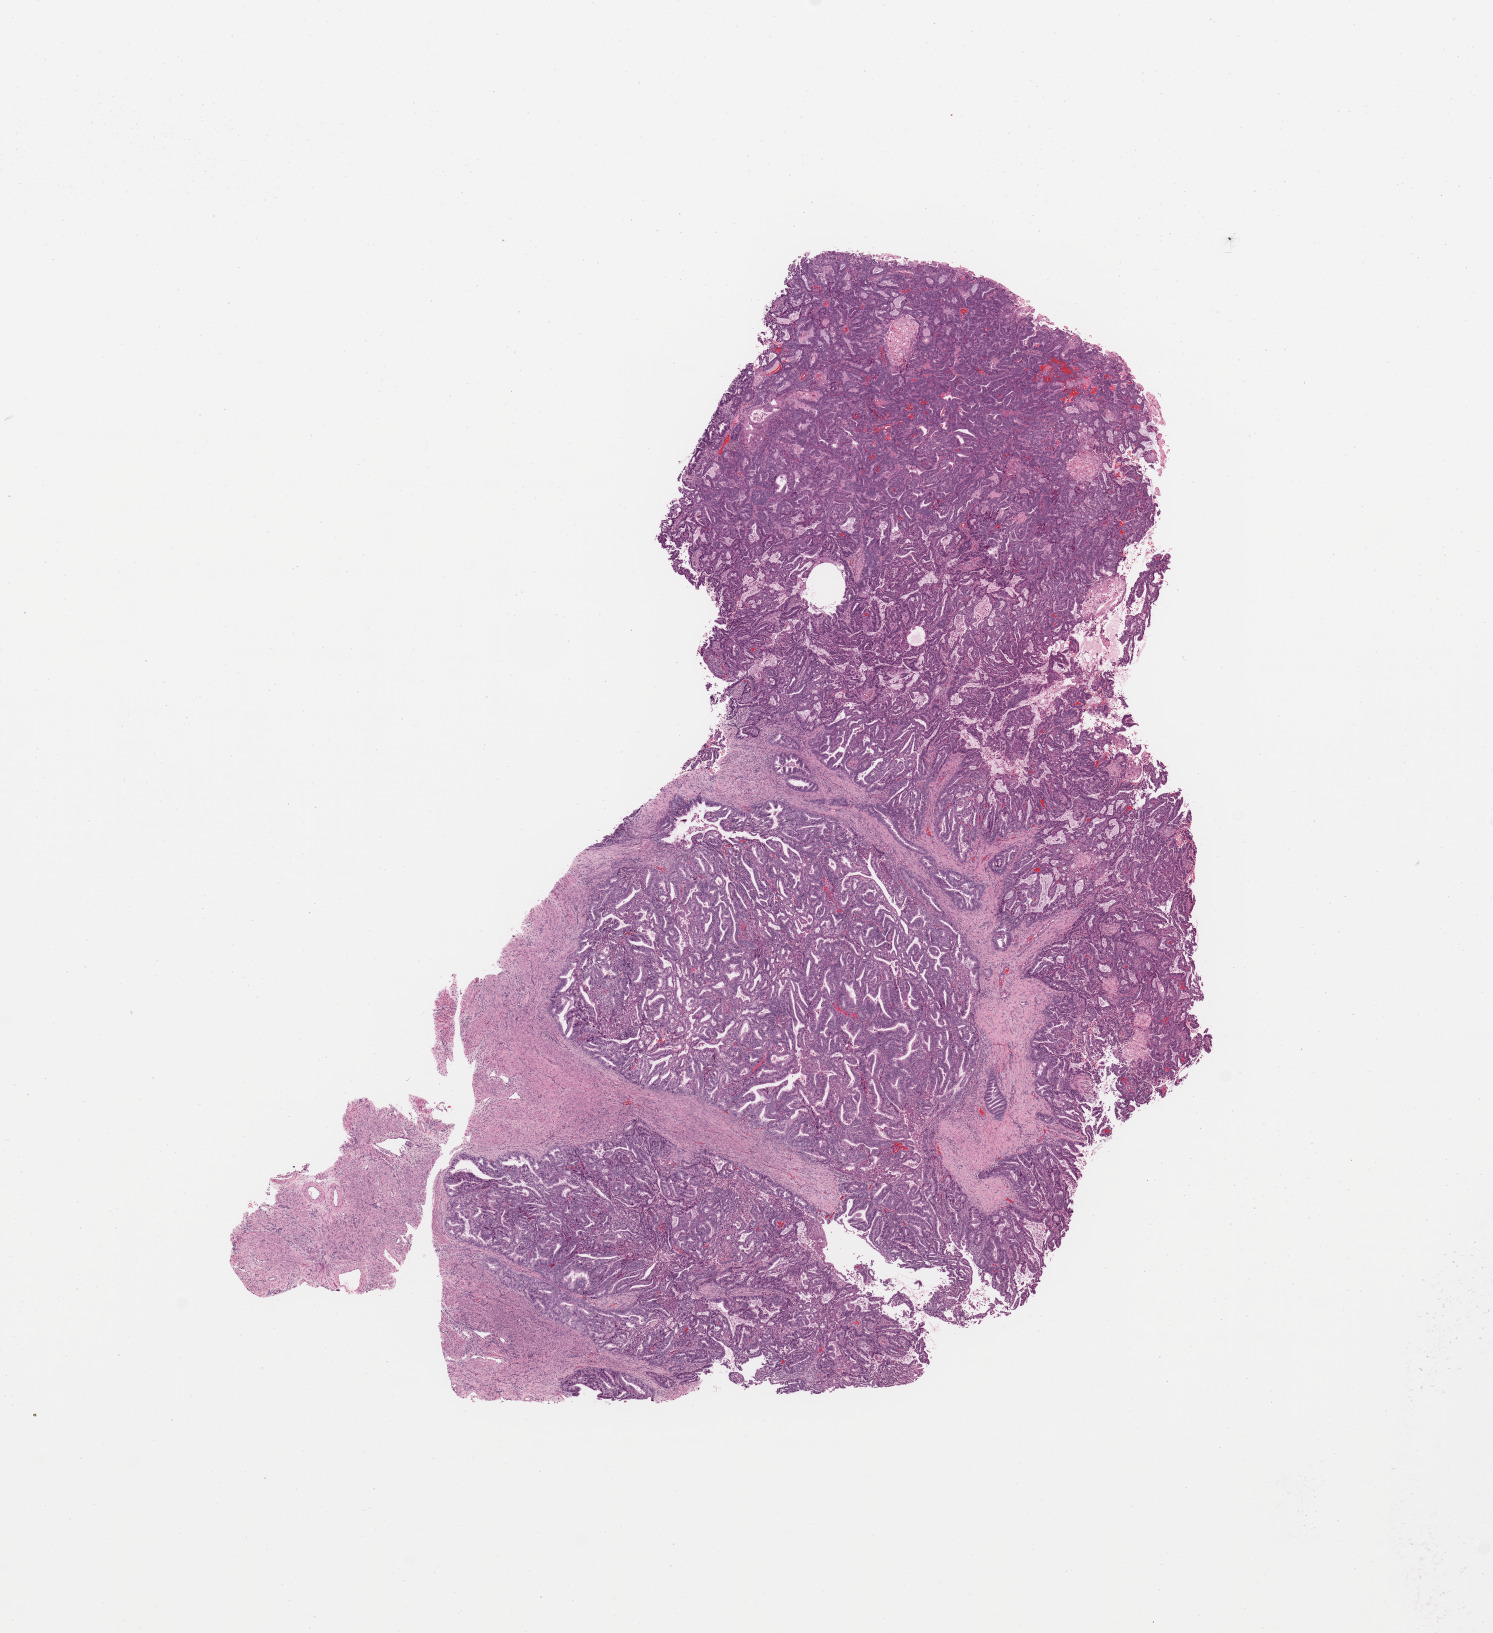
Whole-slide histology image, Hematoxylin and eosin (H&E) stained — shown as a low-resolution overview of the whole scanned area (about 11.8 x 12.9 mm). Tumour tissue sample, sampled site: uterus. Female, 59 y/o. Composition of this section per pathologist review: tumour nuclei 90%, necrosis 0%.
Diagnosis: Endometrioid adenocarcinoma, NOS.